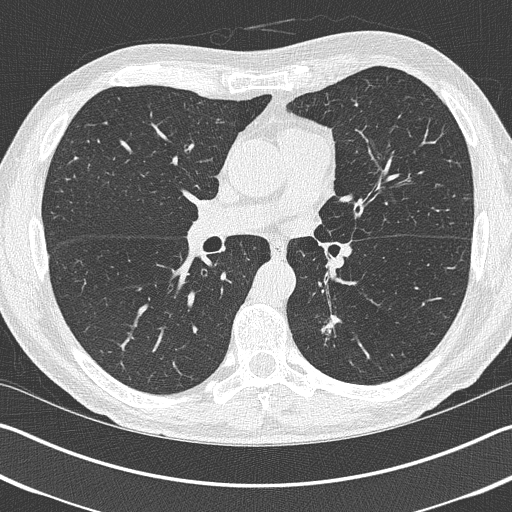
Chest CT (low-dose screening protocol), one axial image, first (baseline) screen, lung window (W 1500 / L -600 HU), lung (sharp) reconstruction kernel (B50f), 120 kVp, slice 177 of 402 in the series, 512 × 512 image matrix. Male, age 69 years at enrolment. Current smoker at enrolment.
Expert reader's lesion annotation, bounding box (x1, y1, x2, y2) in pixels: (293, 304, 350, 363). Screening reader's record for this exam (one nodule recorded; not confirmed to be the boxed lesion): non-calcified nodule or mass ≥4 mm, left upper lobe, 19 × 19 mm, spiculated (stellate) margins, pre-existing on the prior screen: yes. Official screen result: positive, change unspecified: nodule(s) >= 4 mm or enlarging nodule(s), mass(es), or other non-specific abnormalities suspicious for lung cancer. Later outcome: lung cancer diagnosed 202 days after this screen — non-small cell carcinoma, left lower lobe, stage IIIA (AJCC 6th edition), 20 mm at pathology.